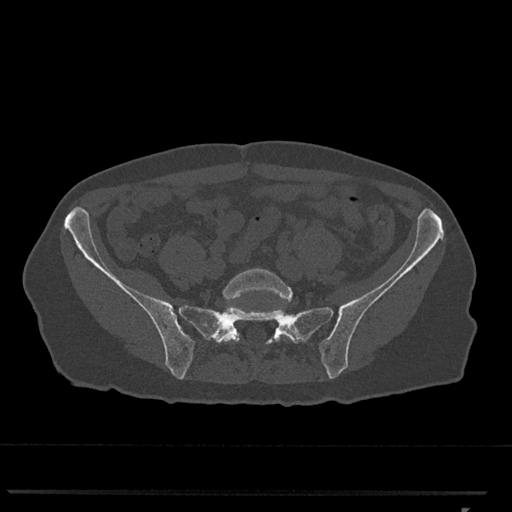
CT including the spine, one axial slice. Position 119 of 793 along the scan axis. Bone window (W 1800 / L 400 HU). 0.5 mm slice thickness. 512 × 512 image matrix, field of view 380 × 380 mm. Female patient, age 62 years. From the clinical record (not read from this slice): primary cancer: renal.
Structures marked on this image (semi-automatically segmented with operator editing):
- L5 vertebra: bounding box (x1, y1, x2, y2) in pixels: (222, 268, 297, 343)